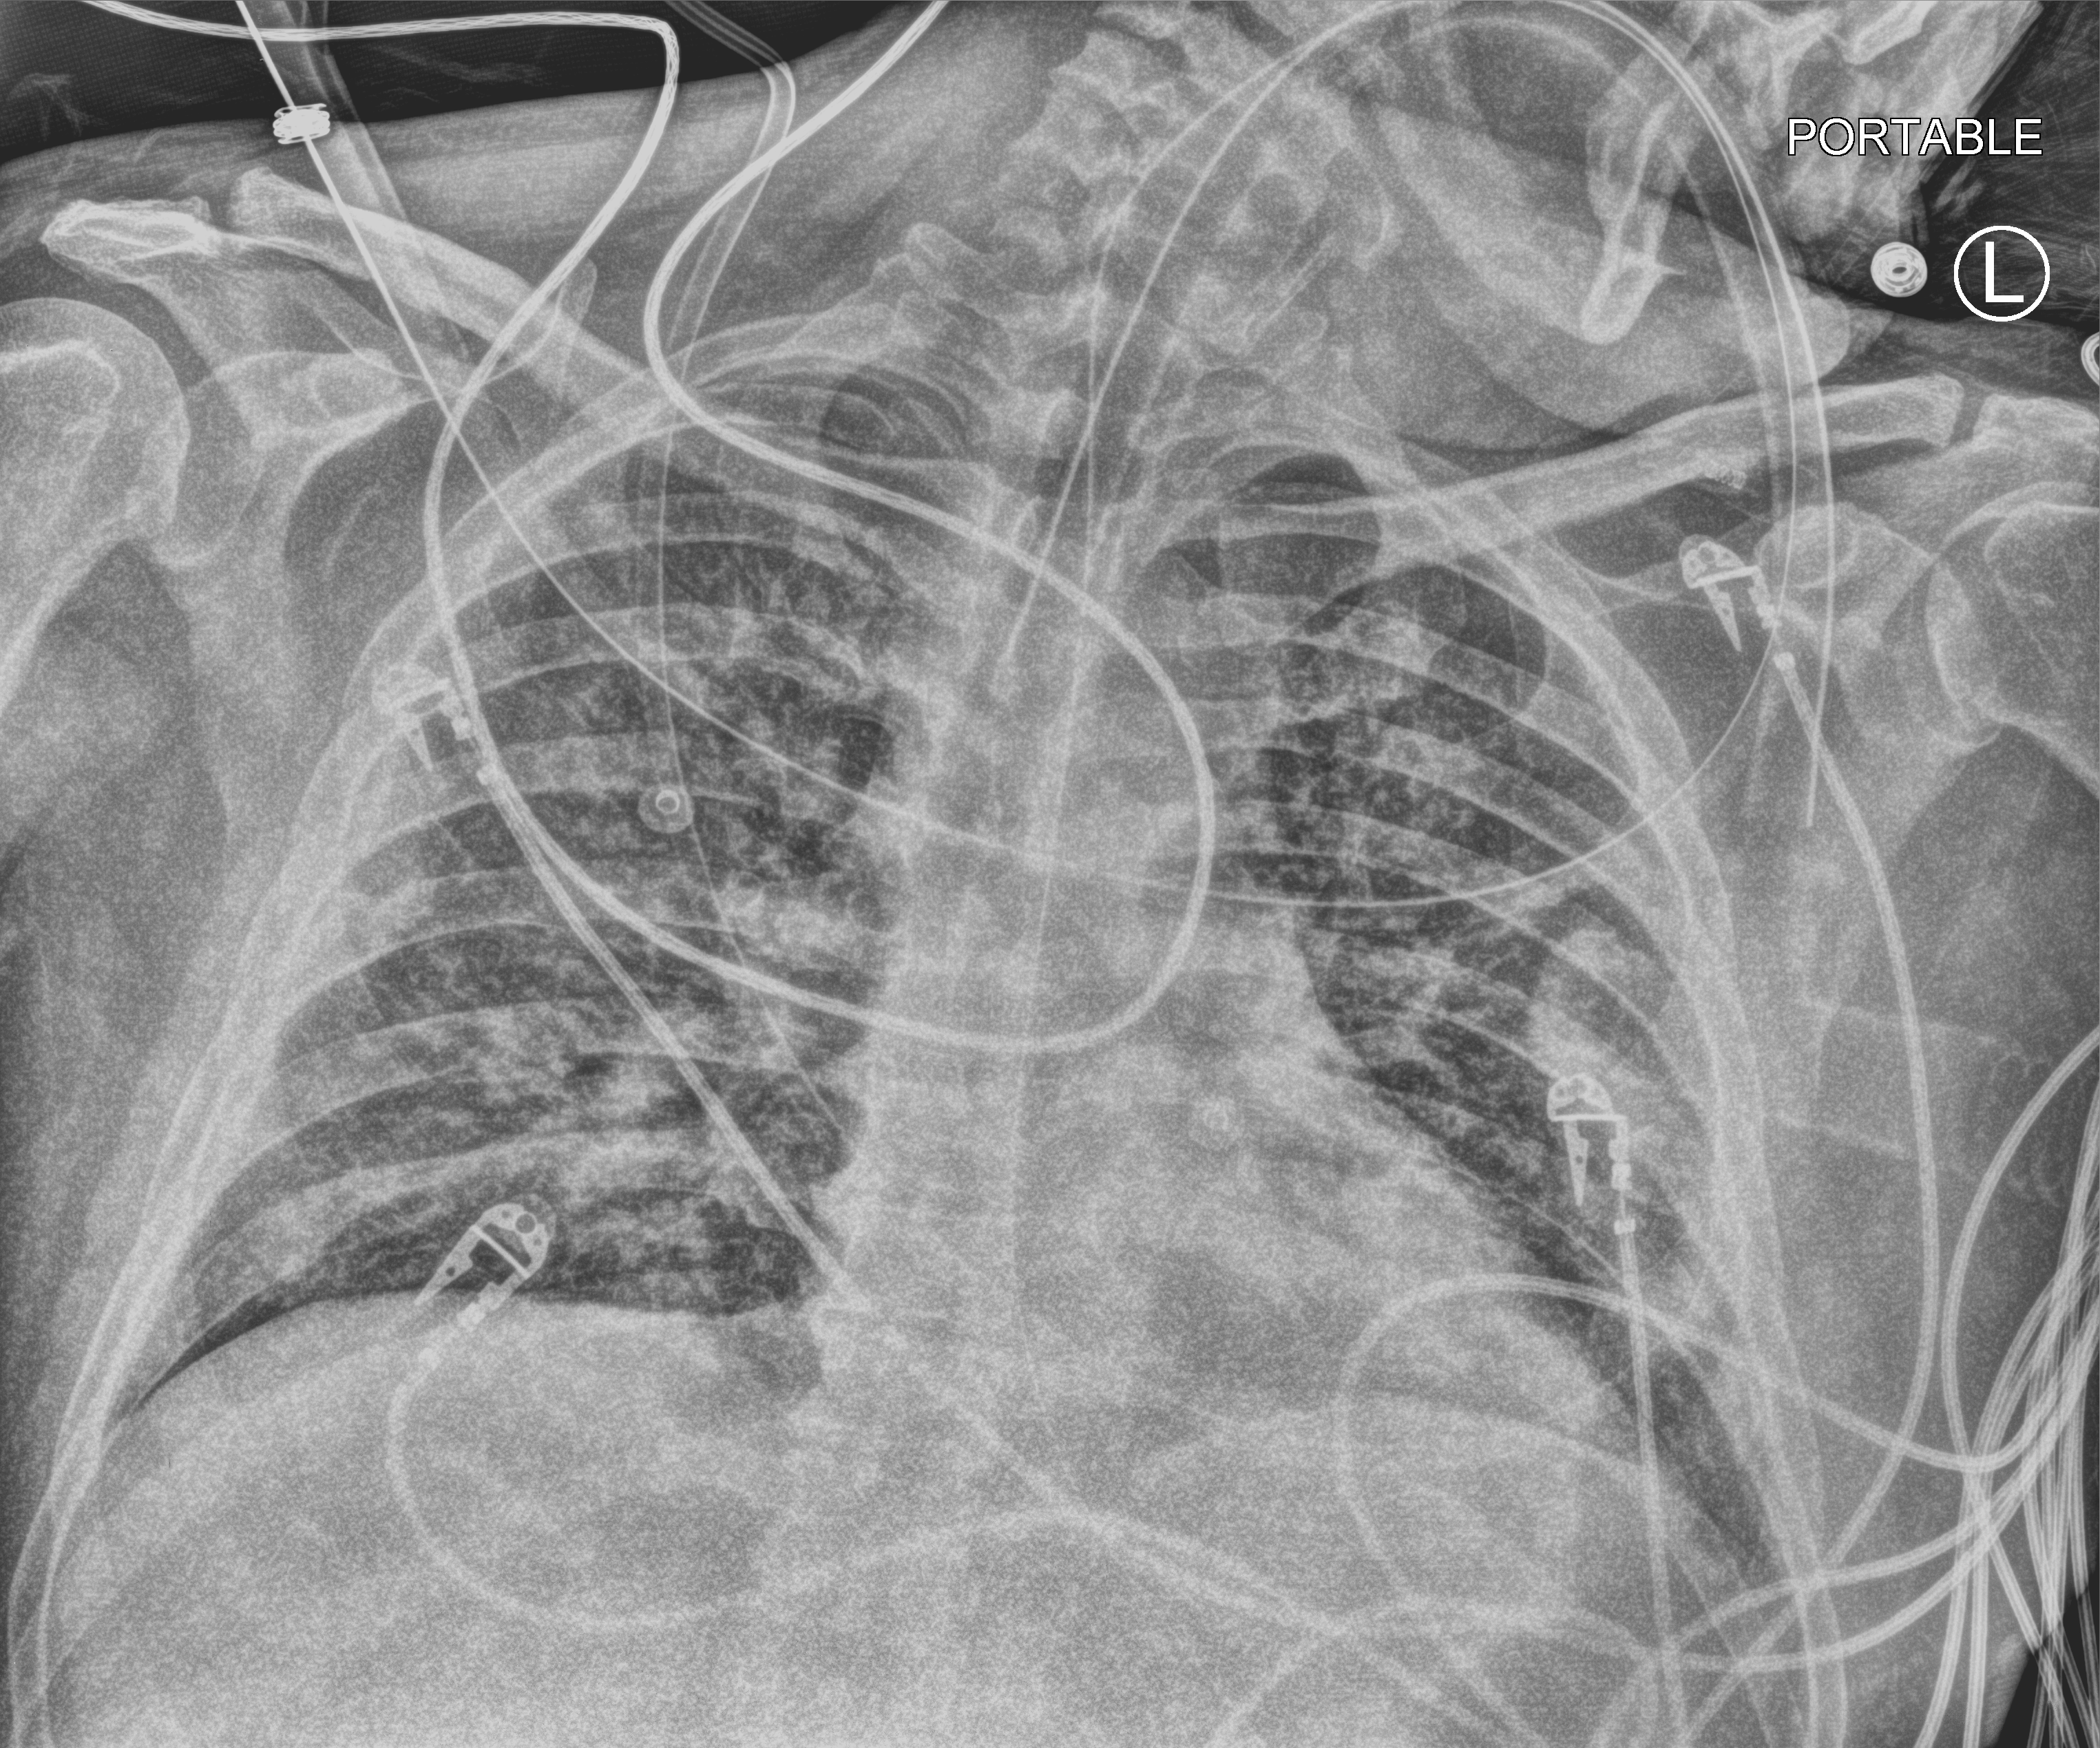
Portable chest radiograph, anteroposterior (AP) projection. Male patient hospitalised with COVID-19, age 18–59 years.
Admission-level facts for this patient (not findings on this image; timing relative to this image not recorded):
- mechanically ventilated during this hospital stay: yes
- other chronic lung disease (admission record): no
- admitted to intensive care during this hospital stay: yes